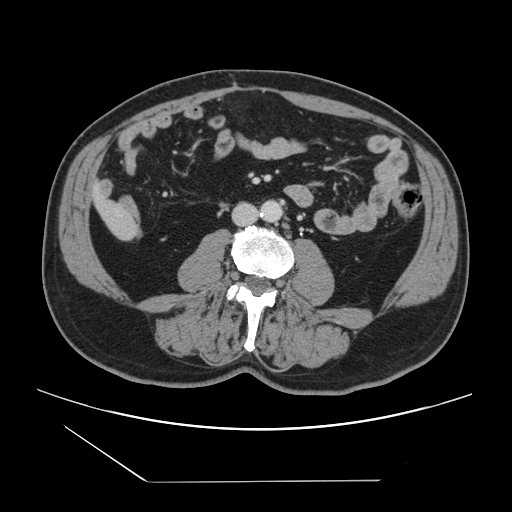
Contrast-enhanced abdominal CT, one axial slice; slice 15 of 157 in the series (ordered by position); intravenous contrast given; soft-tissue window (W 400 / L 40 HU); 2.5 mm slice thickness; 512 × 512 image matrix. Male patient, age 61 years. Case-level facts recorded for this patient, not image findings: diagnosis: colorectal cancer liver metastases, imaged before liver resection.
Annotated regions visible in this slice (manually delineated by an expert):
- liver: bounding box [x1, y1, x2, y2] px = [96, 197, 136, 240]
- planned liver remnant (the part of the liver to remain after resection): [96, 194, 119, 217]